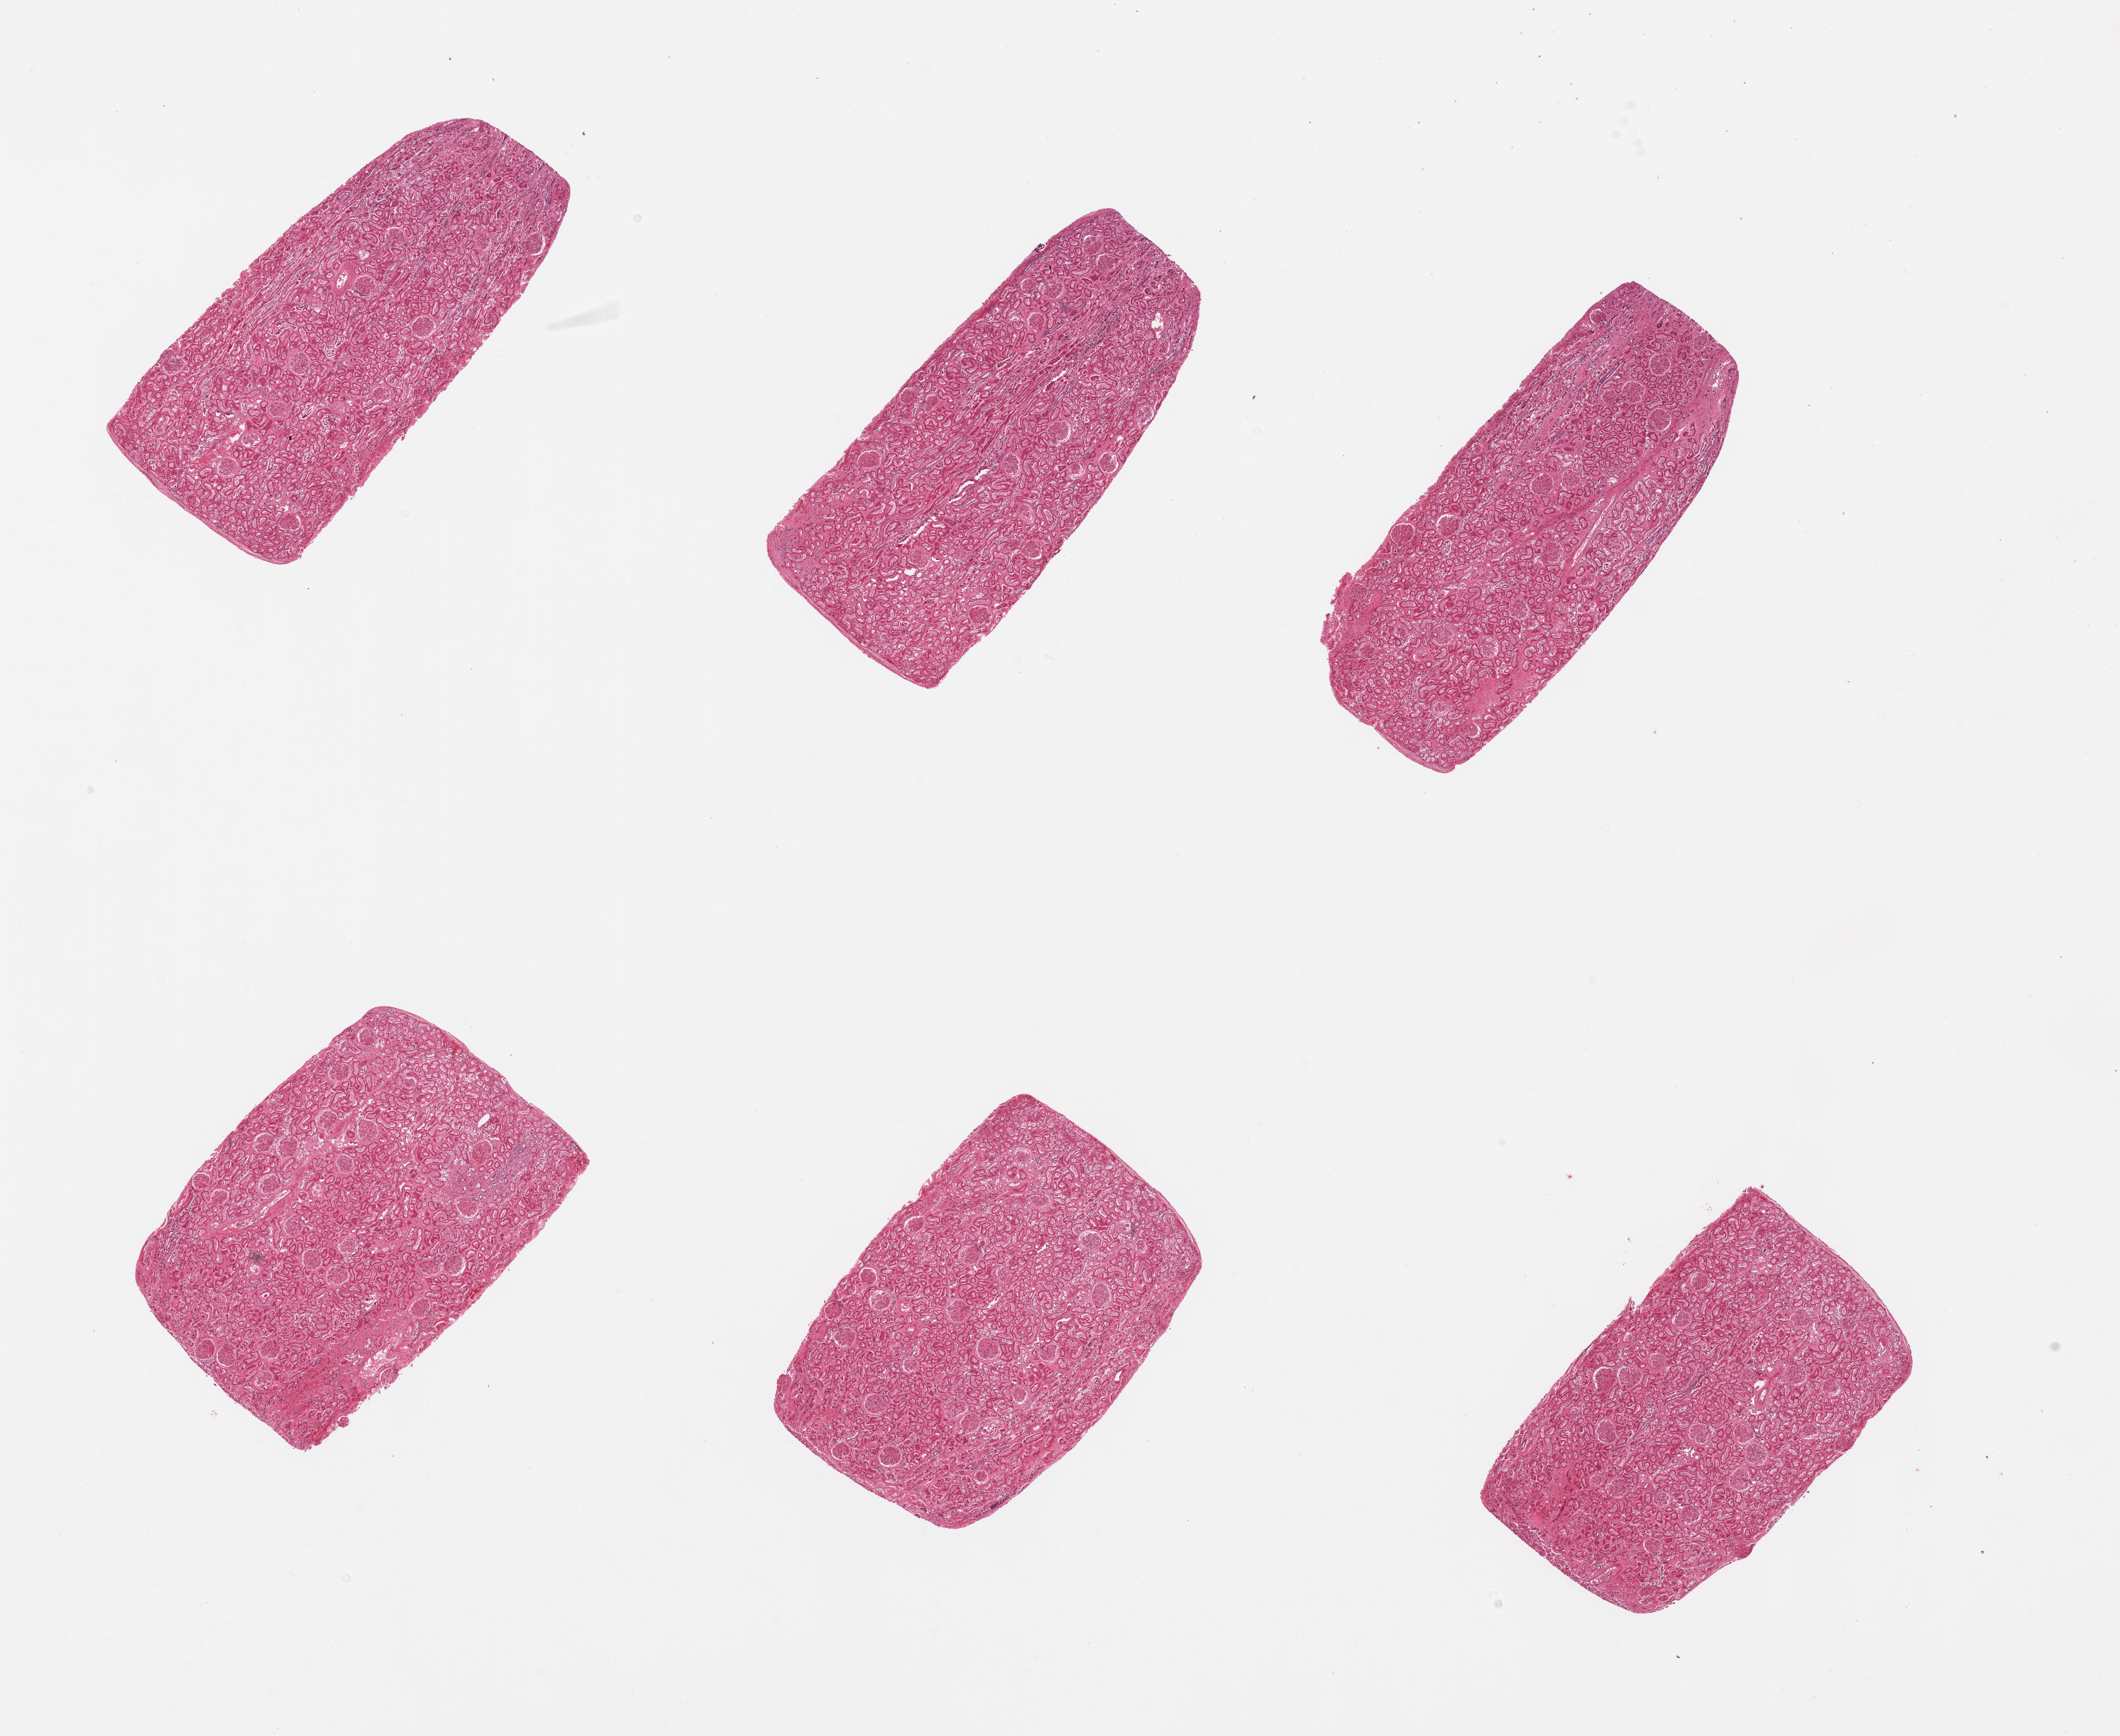
Haematoxylin and eosin whole-slide image, shown as a low-resolution overview of the whole scanned area (about 23.6 x 19.3 mm); PAXgene-fixed, paraffin-embedded tissue; section of renal cortex (target tissue); donor tissue sample. Male donor.
Review note (as recorded): 6 pieces, glomeruli in all sections.